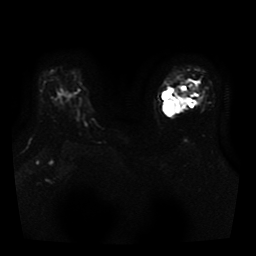
Breast MRI, one axial slice; slice 29 of 41 in the series (ordered by position); diffusion-weighted series; image 2 of 3 stored at this slice position (different b-values; order by instance number); 1.5 T; 5 mm slice thickness; 256 × 256 image matrix, field of view 330 × 330 mm. Female patient.
Outlined on this slice (outlined manually by an expert reader):
- tumour on diffusion-weighted imaging: bounding box <162,91,185,115> (left, top, right, bottom; pixels)